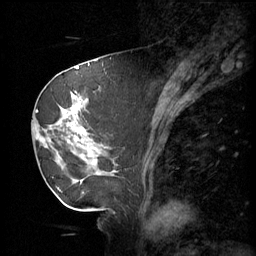
Breast MRI (dynamic contrast-enhanced), one sagittal slice. Position 23 of 60 along the scan axis. 3 images stored at this slice position (order not interpretable as contrast timing). 1.5 T. TE 4.2 ms, TR 11 ms. 2 mm slice thickness. 256 × 256 image matrix, field of view 220 × 220 mm. Female patient, age 69 years.
Outlined on this slice (semi-automatically segmented with operator editing):
- analysis volume of interest (the breast-tissue region the enhancement analysis was run in; not a lesion): bounding box [x1, y1, x2, y2] px = [36, 88, 116, 189]
- tumour enhancement mask (voxels above the 70 % enhancement threshold inside the analysis volume of interest): [37, 94, 99, 183]